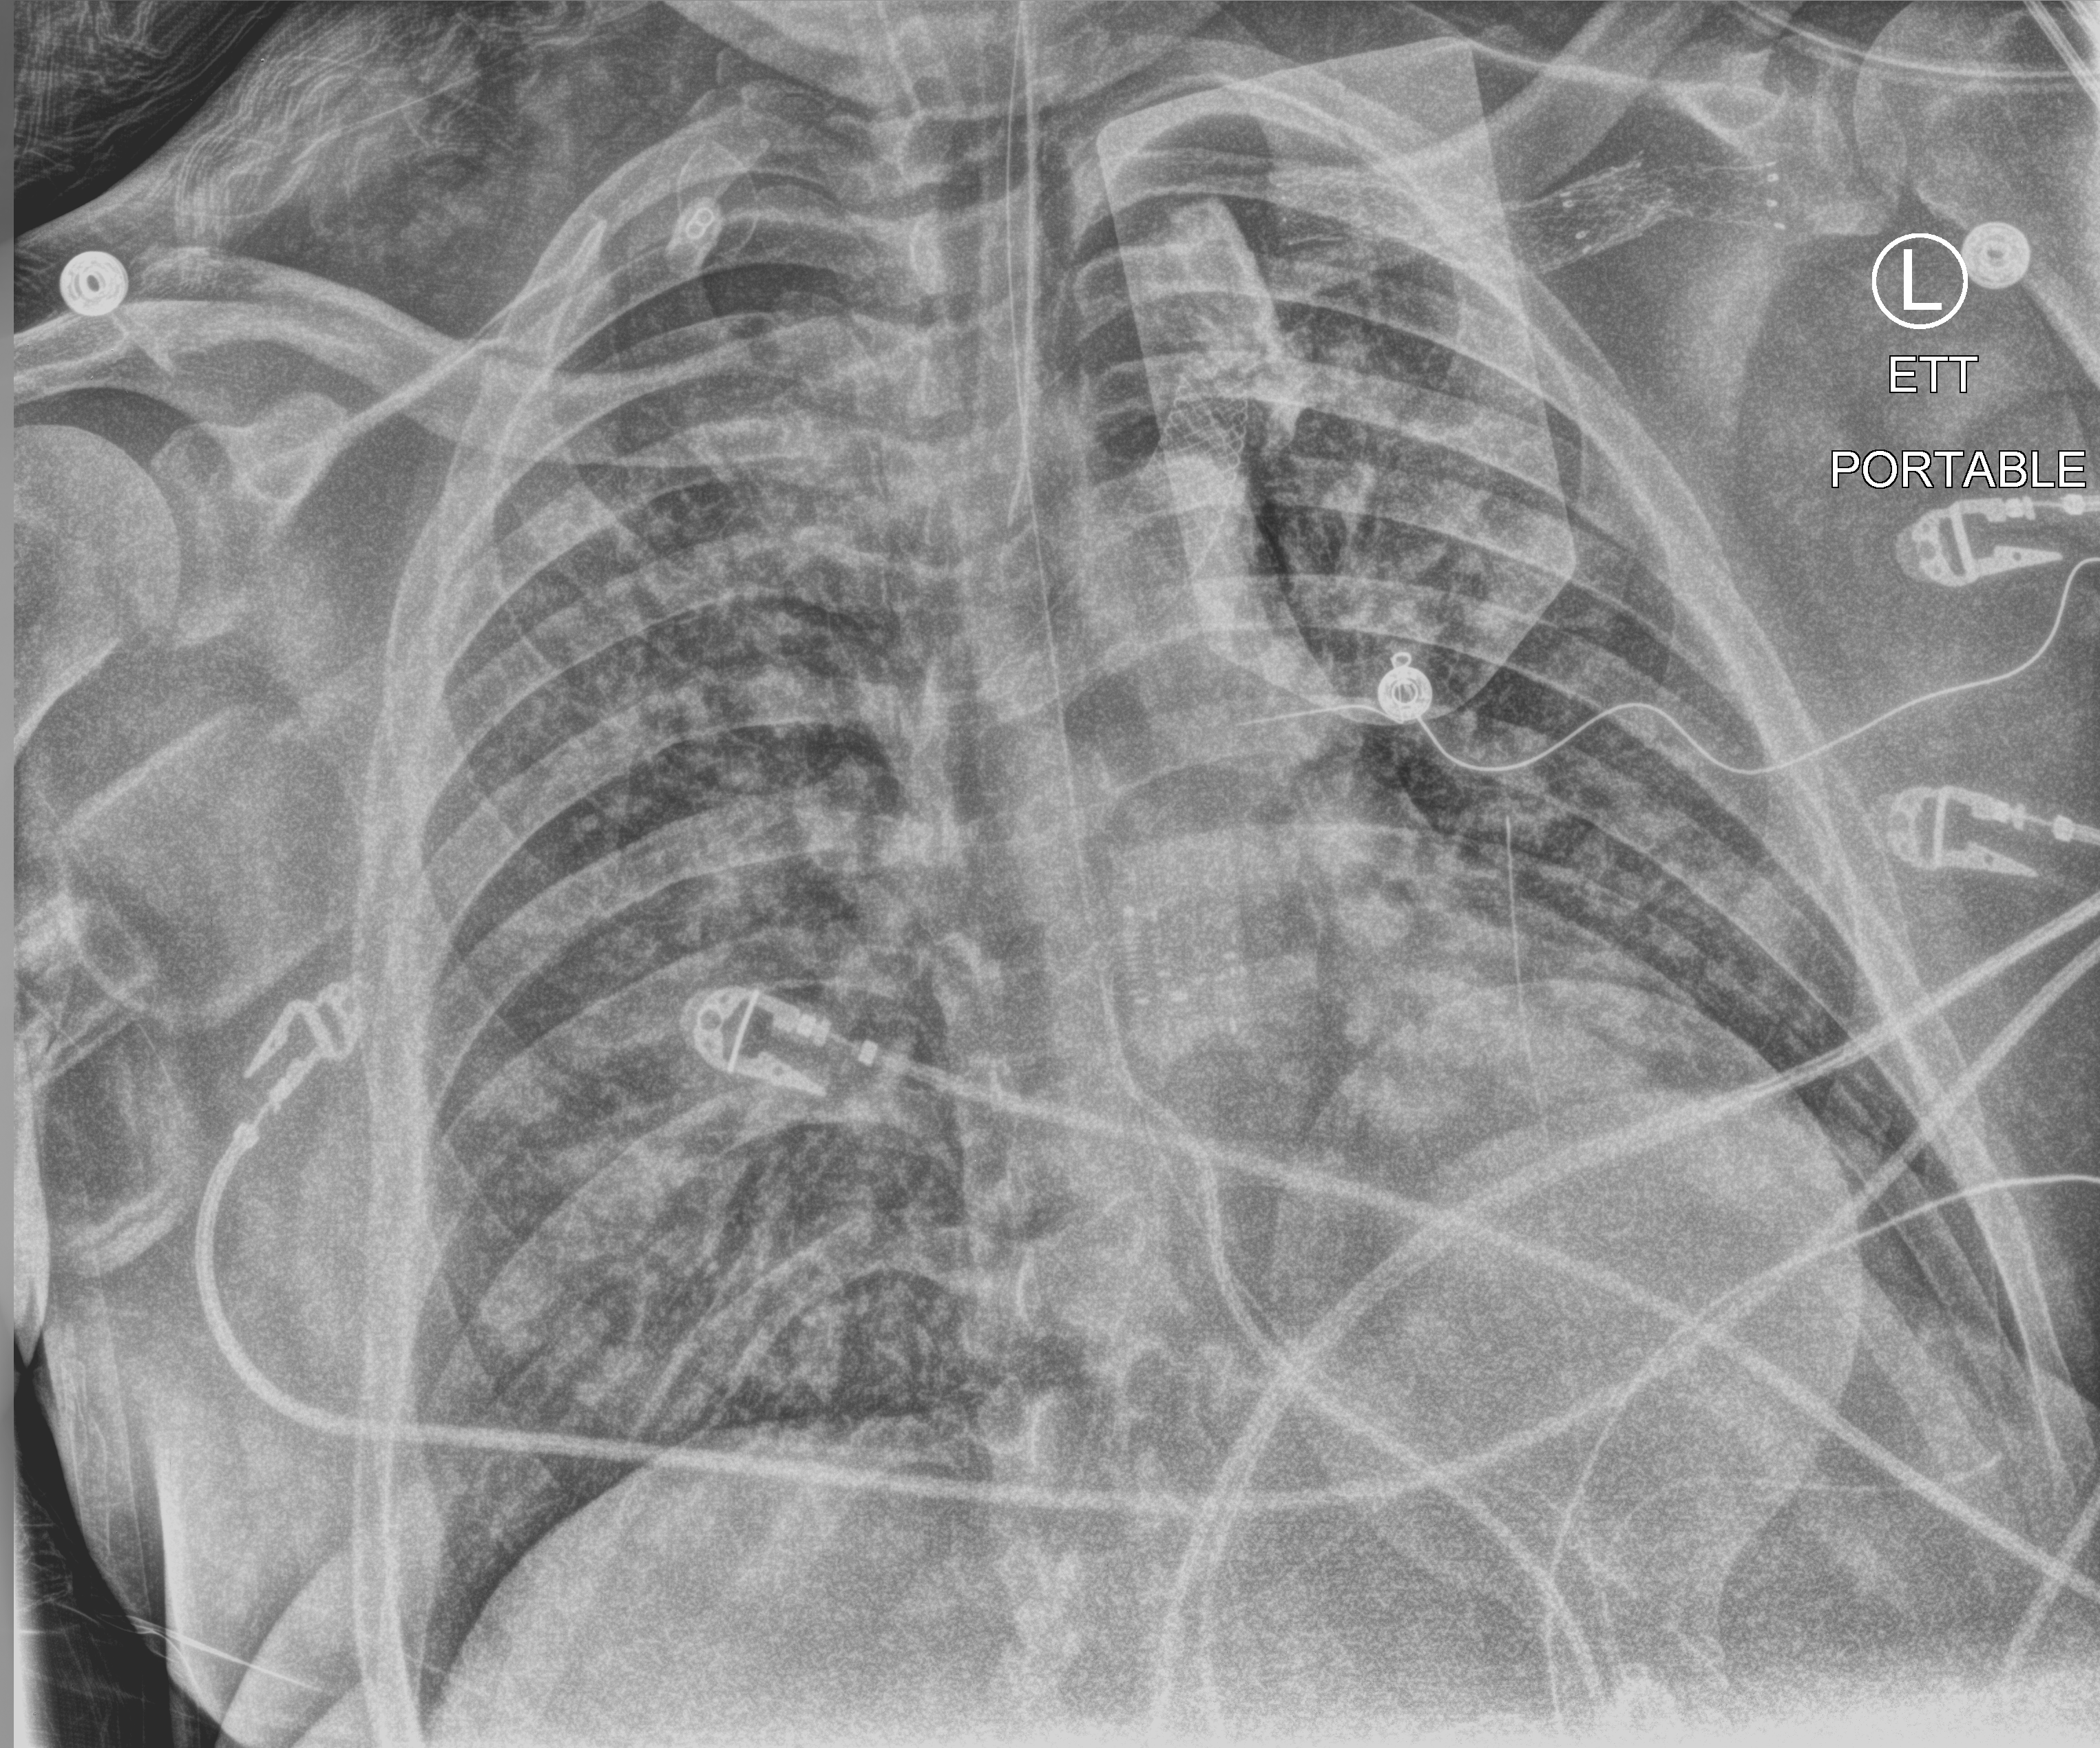
Portable chest radiograph, anteroposterior (AP) projection. Patient hospitalised with COVID-19; male, aged 18–59 years.
From the hospital-stay record, not from the radiograph (when in the stay this image was taken is not recorded): admitted to intensive care during this hospital stay: yes.